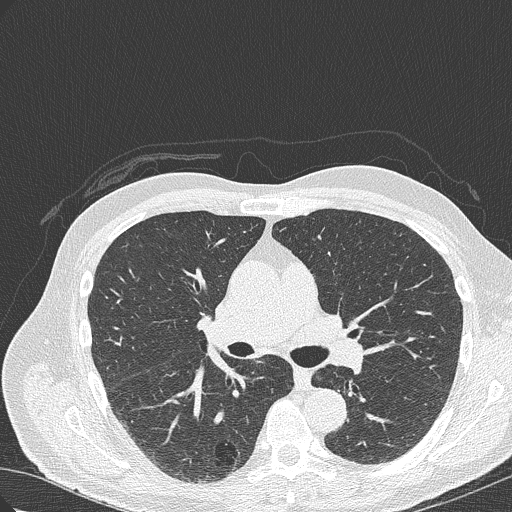
Chest CT (low-dose screening protocol), one axial image. Baseline annual screen. Lung window (W 1500 / L -600 HU). 120 kVp. Slice 131 of 322 in the series. Male participant, aged 70 years at enrolment.
• Expert-annotated lung lesion, bounding box <199,419,263,474> (left, top, right, bottom; pixels).
• The screening reader recorded 4 non-calcified nodules or masses ≥4 mm on this exam (right lower lobe, right lower lobe, right upper lobe, right lower lobe); which of them this box marks is not recorded.
• Official screen result: positive, change unspecified: nodule(s) >= 4 mm or enlarging nodule(s), mass(es), or other non-specific abnormalities suspicious for lung cancer.